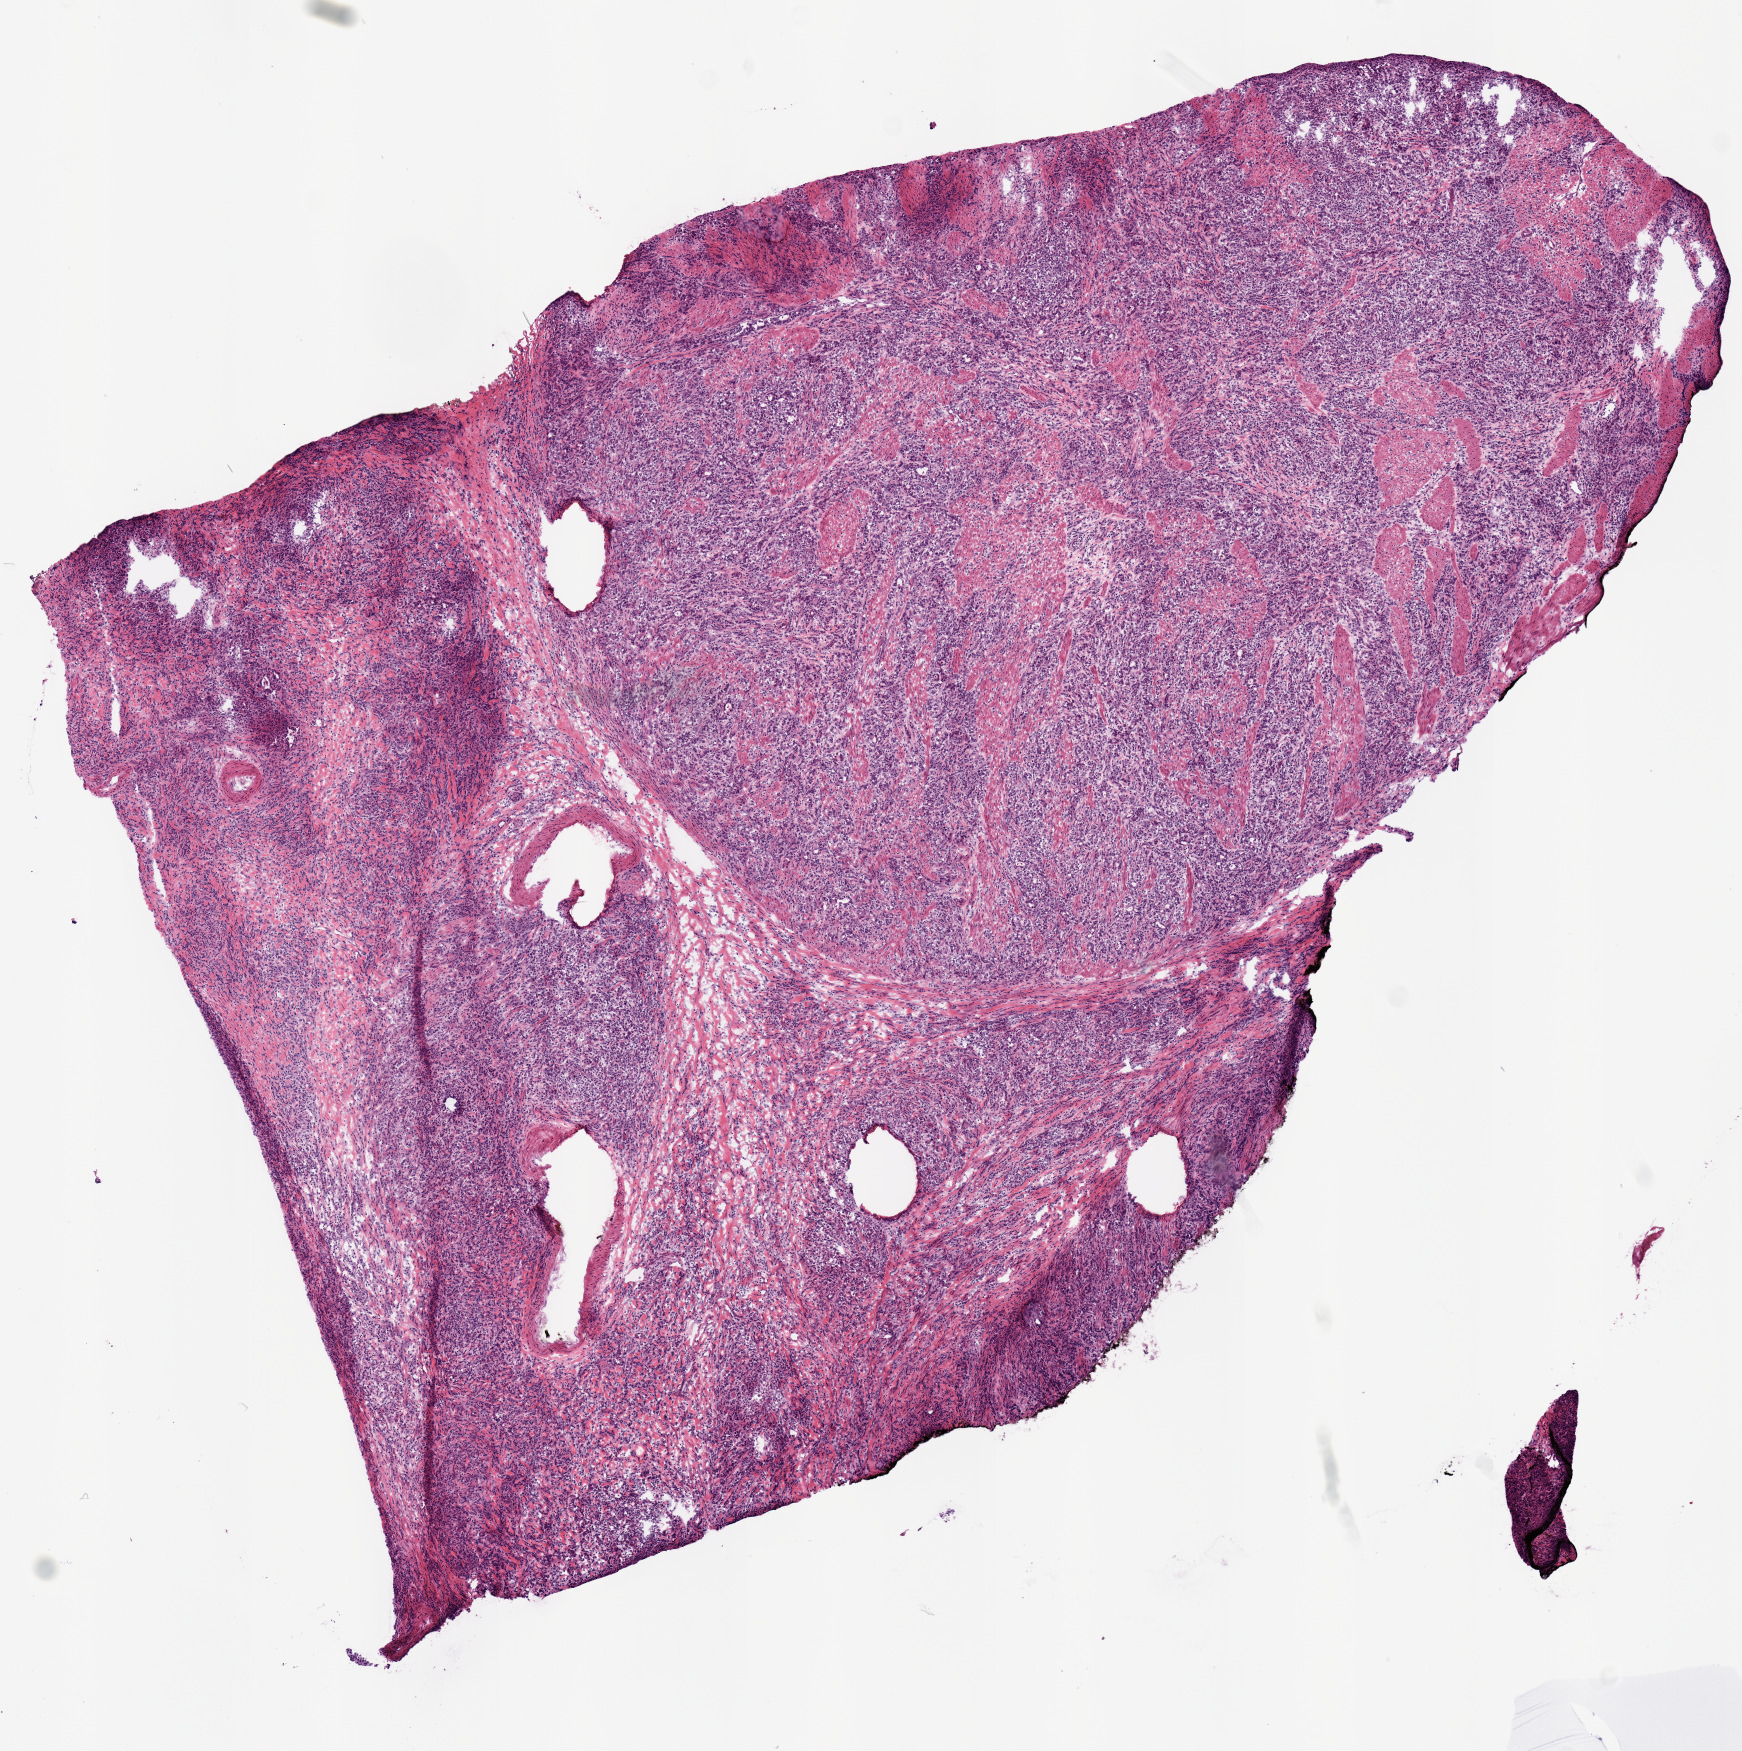
Whole-slide histology image, Hematoxylin and eosin (H&E) stained, whole scanned area (about 6.9 x 6.9 mm, acquisition: 20x scan) shown as a low-resolution overview; frozen section; sample: primary tumour, stomach. Patient: male, age at initial diagnosis 77 years.
Histologic diagnosis: Carcinoma, diffuse type (body of stomach).